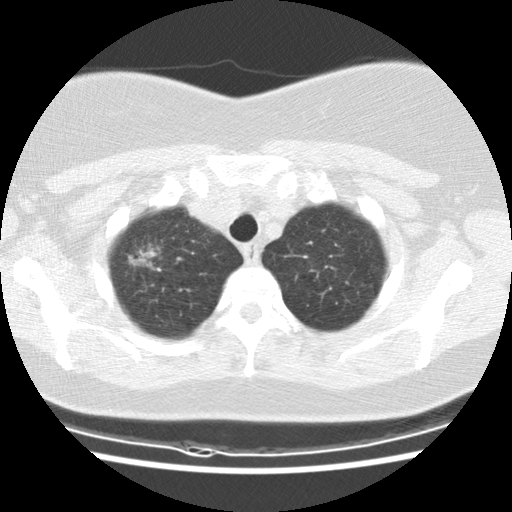
Chest CT (low-dose screening protocol), one axial image; baseline annual screen; lung window (W 1500 / L -600 HU); standard (soft-tissue) reconstruction kernel (STANDARD); 120 kVp. Female participant, aged 61 years at enrolment. Former smoker at enrolment.
Expert-annotated lung lesion, bounding box <114,230,178,287> (left, top, right, bottom; pixels). The exam's reader record, not a measurement of the box and not confirmed to be the same lesion: non-calcified nodule or mass ≥4 mm, right upper lobe, 26 × 16 mm, spiculated (stellate) margins, mixed attenuation. Official screen result: positive, change unspecified: nodule(s) >= 4 mm or enlarging nodule(s), mass(es), or other non-specific abnormalities suspicious for lung cancer. Participant outcome: lung cancer diagnosed 47 days after this screen — bronchiolo-alveolar carcinoma, mixed mucinous and non-mucinous, right upper lobe, well differentiated (G1), stage IA (AJCC 6th edition), 25 mm at pathology.